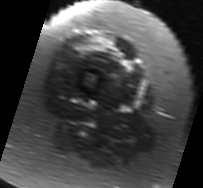
MRI of an extremity soft-tissue mass, one axial slice. Position 14 of 91 along the scan axis. T2-weighted fat-saturated. MR volume resampled by the dataset authors to the PET/CT grid (not the native acquisition matrix). 3.27 mm slice thickness. 203 × 188 image matrix, field of view 198 × 184 mm. Female patient. From the clinical record (not read from this slice): histological type: malignant solitary fibrous tumor; grade: intermediate; site of the primary tumour: right thigh.
Structures marked on this image (expert contour drawn on MRI and transferred to this co-registered scan by the dataset authors):
- gross tumour volume including surrounding oedema: bounding box <81,35,134,70> (left, top, right, bottom; pixels)